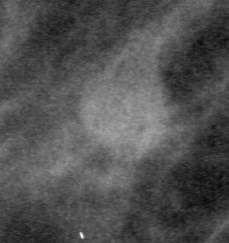
Cropped region of a digitized screen-film mammogram centred on a radiologist-marked abnormality; left breast; MLO view; BI-RADS breast density category 2 (scale 1–4).
Marked abnormality: mass, shape lobulated, margins ill defined; BI-RADS assessment category 4; pathology result (as recorded, not read from the image): benign.